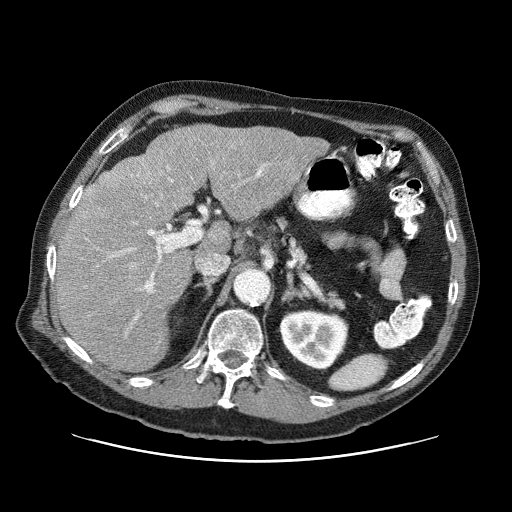
Contrast-enhanced abdominal CT (liver protocol), one axial slice; position 43 of 87 along the scan axis; reconstruction kernel STANDARD; 120 kVp; one of 3 acquisitions stored at this slice position; soft-tissue window (W 400 / L 40 HU); 2.5 mm slice thickness; 512 × 512 image matrix. From the clinical record (not read from this slice): diagnosis: hepatocellular carcinoma (patient treated with transarterial chemoembolisation; whether this scan precedes or follows treatment is not stated here); TNM stage (as recorded): Stage-IIIA; Child-Pugh class: A; tumour differentiation: well differentiated; tumour nodularity: multinodular.
Structures marked on this image (semi-automatically segmented with operator editing):
- liver parenchyma outside the tumour (the mass and vessels are separate outlines, so this box may not span the whole liver): bounding box [x1, y1, x2, y2] px = [56, 124, 329, 372]
- liver vessels: [87, 163, 265, 320]